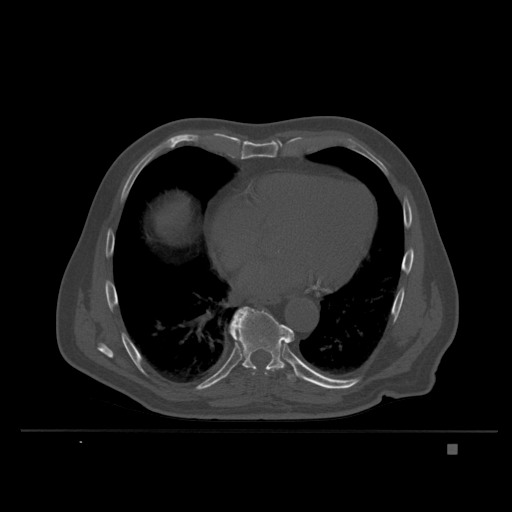
CT including the spine, one axial slice. Bone window (W 1800 / L 400 HU). 1.5 mm slice thickness. 512 × 512 image matrix. Patient: male, 73 years. Case-level facts recorded for this patient, not image findings: primary cancer: skin.
Annotated regions visible in this slice (semi-automatically segmented with operator editing):
- T8 vertebra: bounding box [x1, y1, x2, y2] px = [253, 373, 268, 375]
- T9 vertebra: [229, 307, 303, 384]